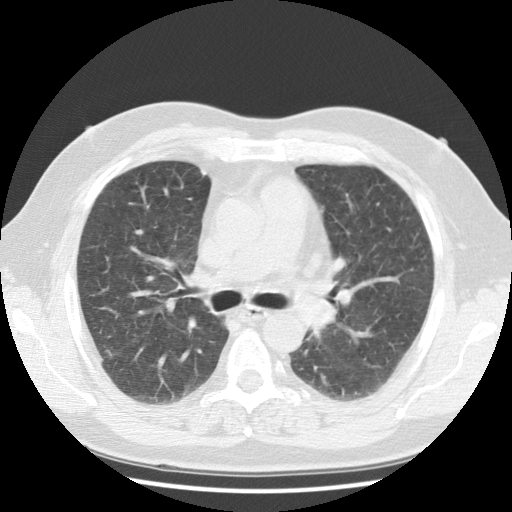
Low-dose screening chest CT, one axial slice; slice 69 of 108 in the series (ordered by position); lung window (W 1500 / L -600 HU); 512 × 512 image matrix.
Annotated regions visible in this slice (outlined manually by an expert reader):
- lesion 1 (tumor, hilum of left lung): bounding box [x1, y1, x2, y2] px = [304, 296, 336, 330]